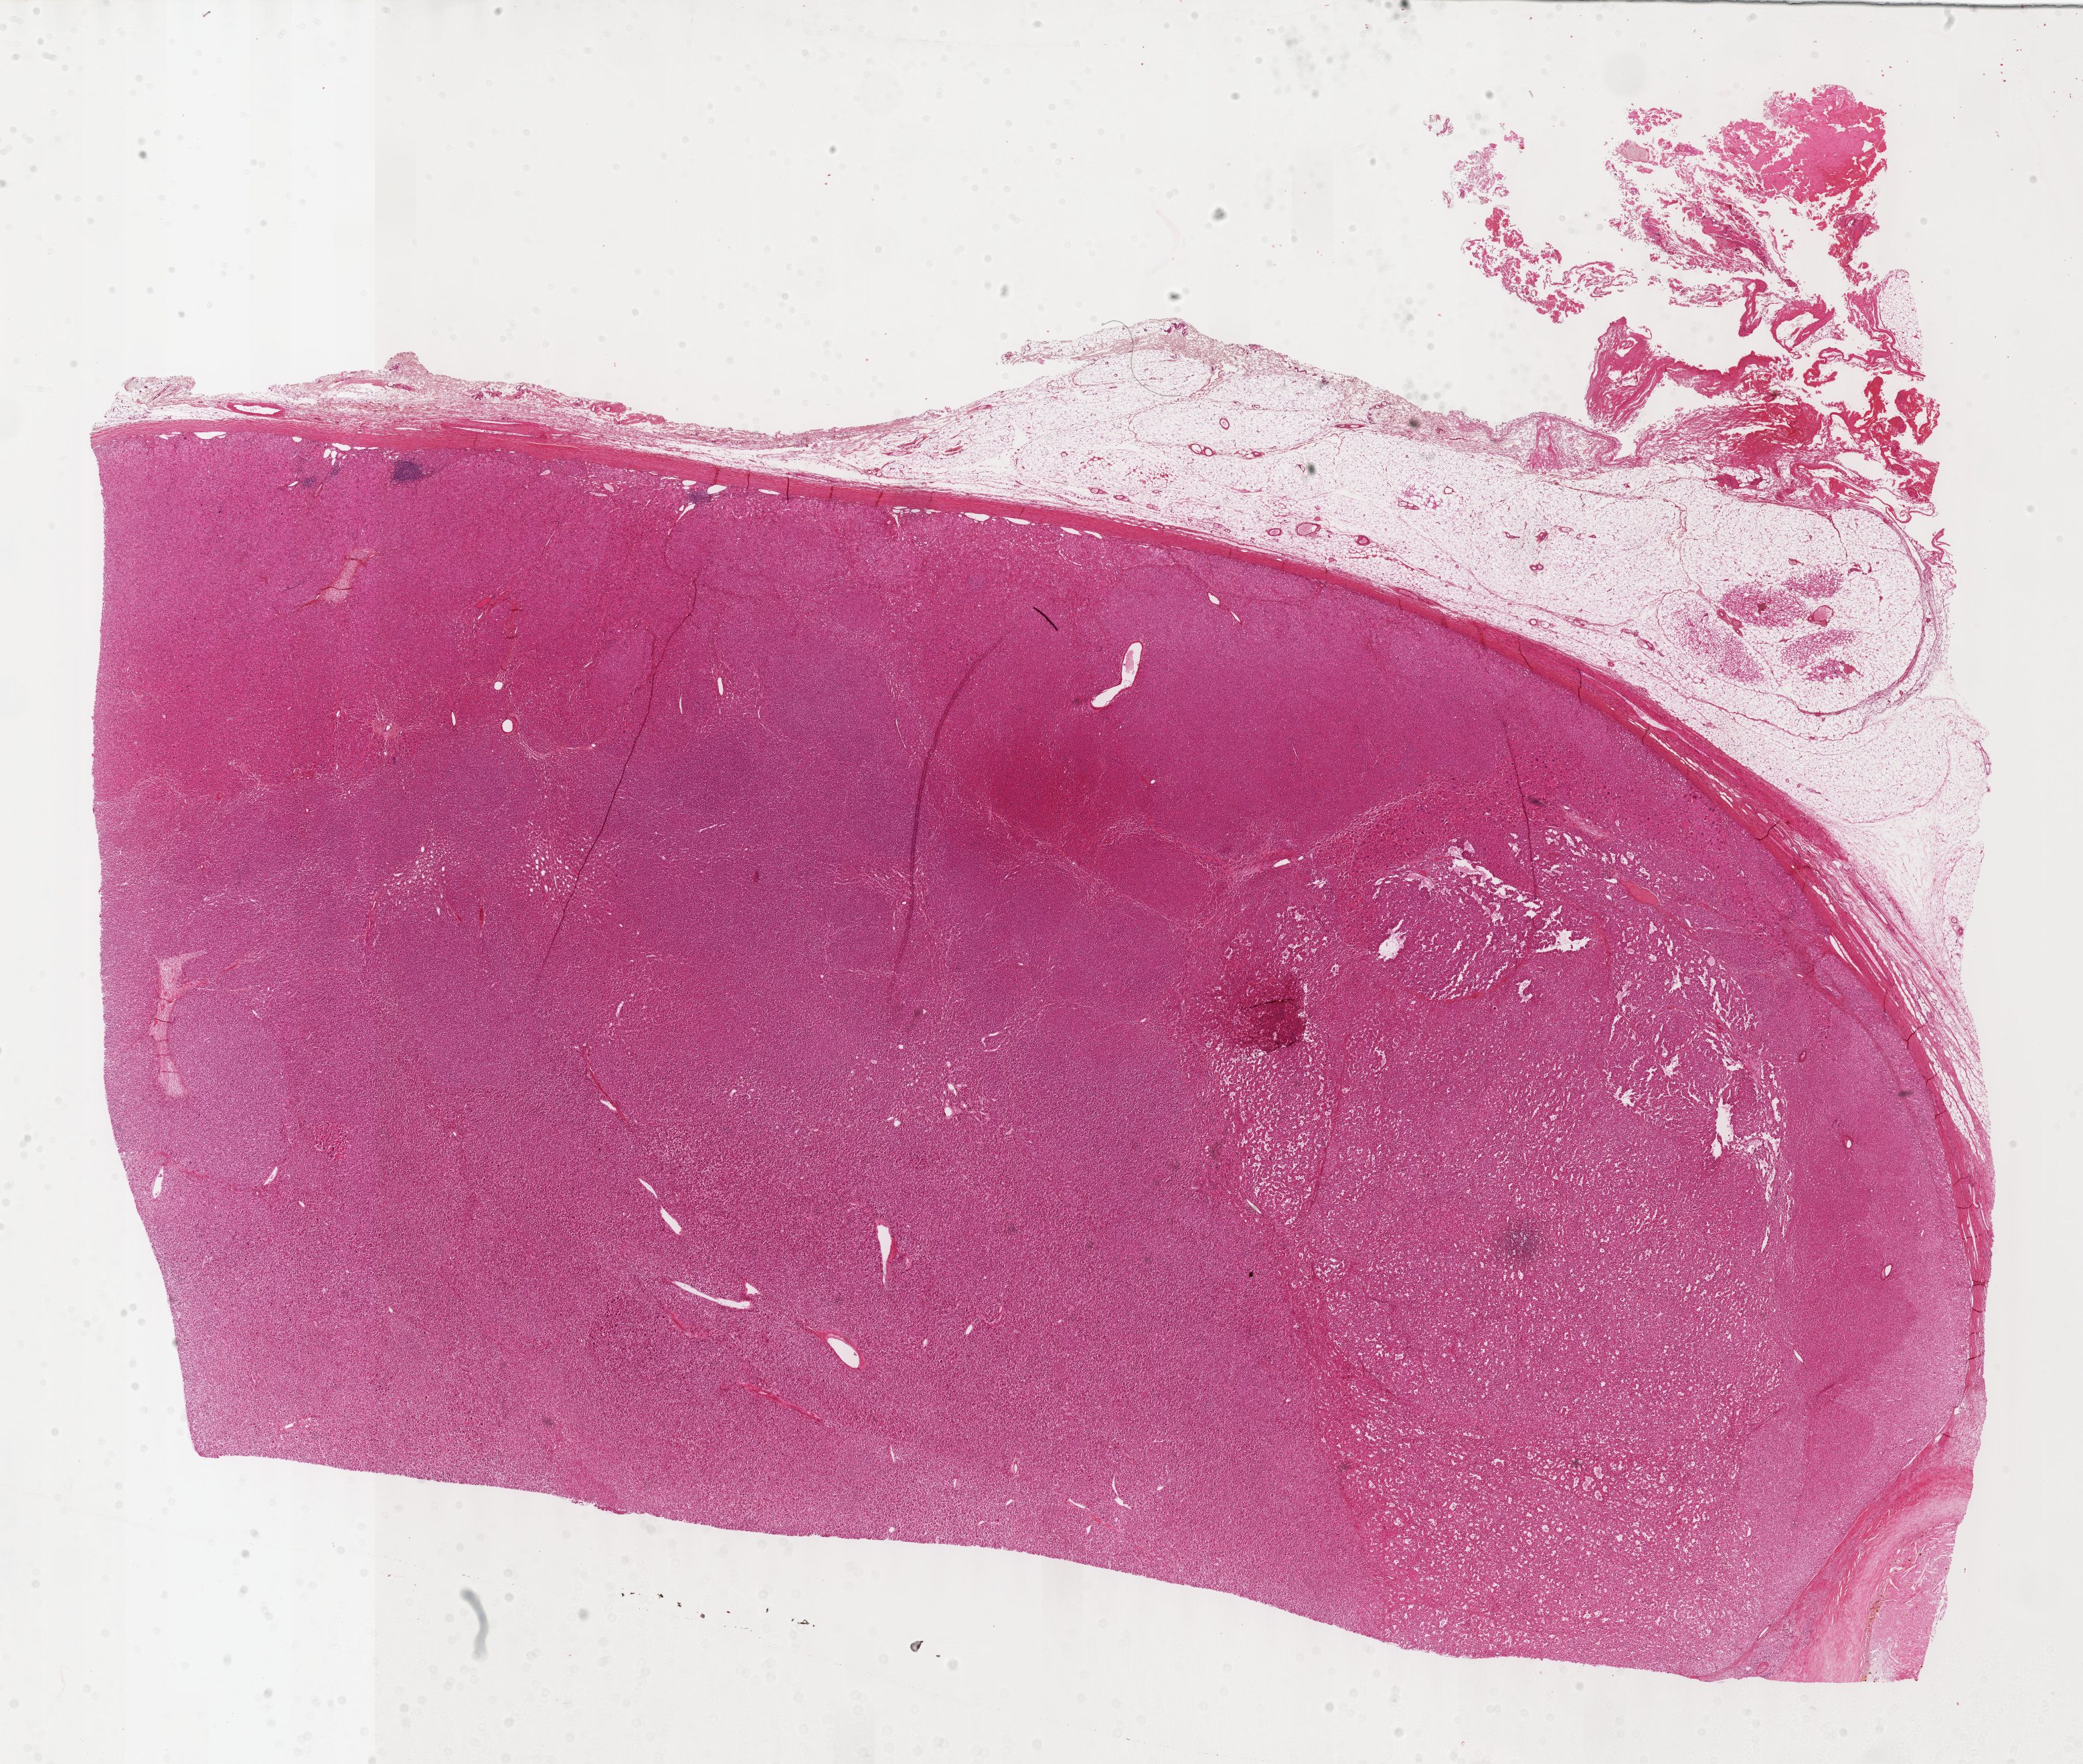
H&E whole-slide image, a low-resolution overview of the entire scanned area, about 25.1 x 21.3 mm (acquisition: 40x scan); formalin-fixed paraffin-embedded (FFPE) diagnostic section; sample: primary tumour, adrenal cortex. Patient: female, age at initial diagnosis 30 years.
Histologic diagnosis: Adrenal cortical carcinoma (cortex of adrenal gland).